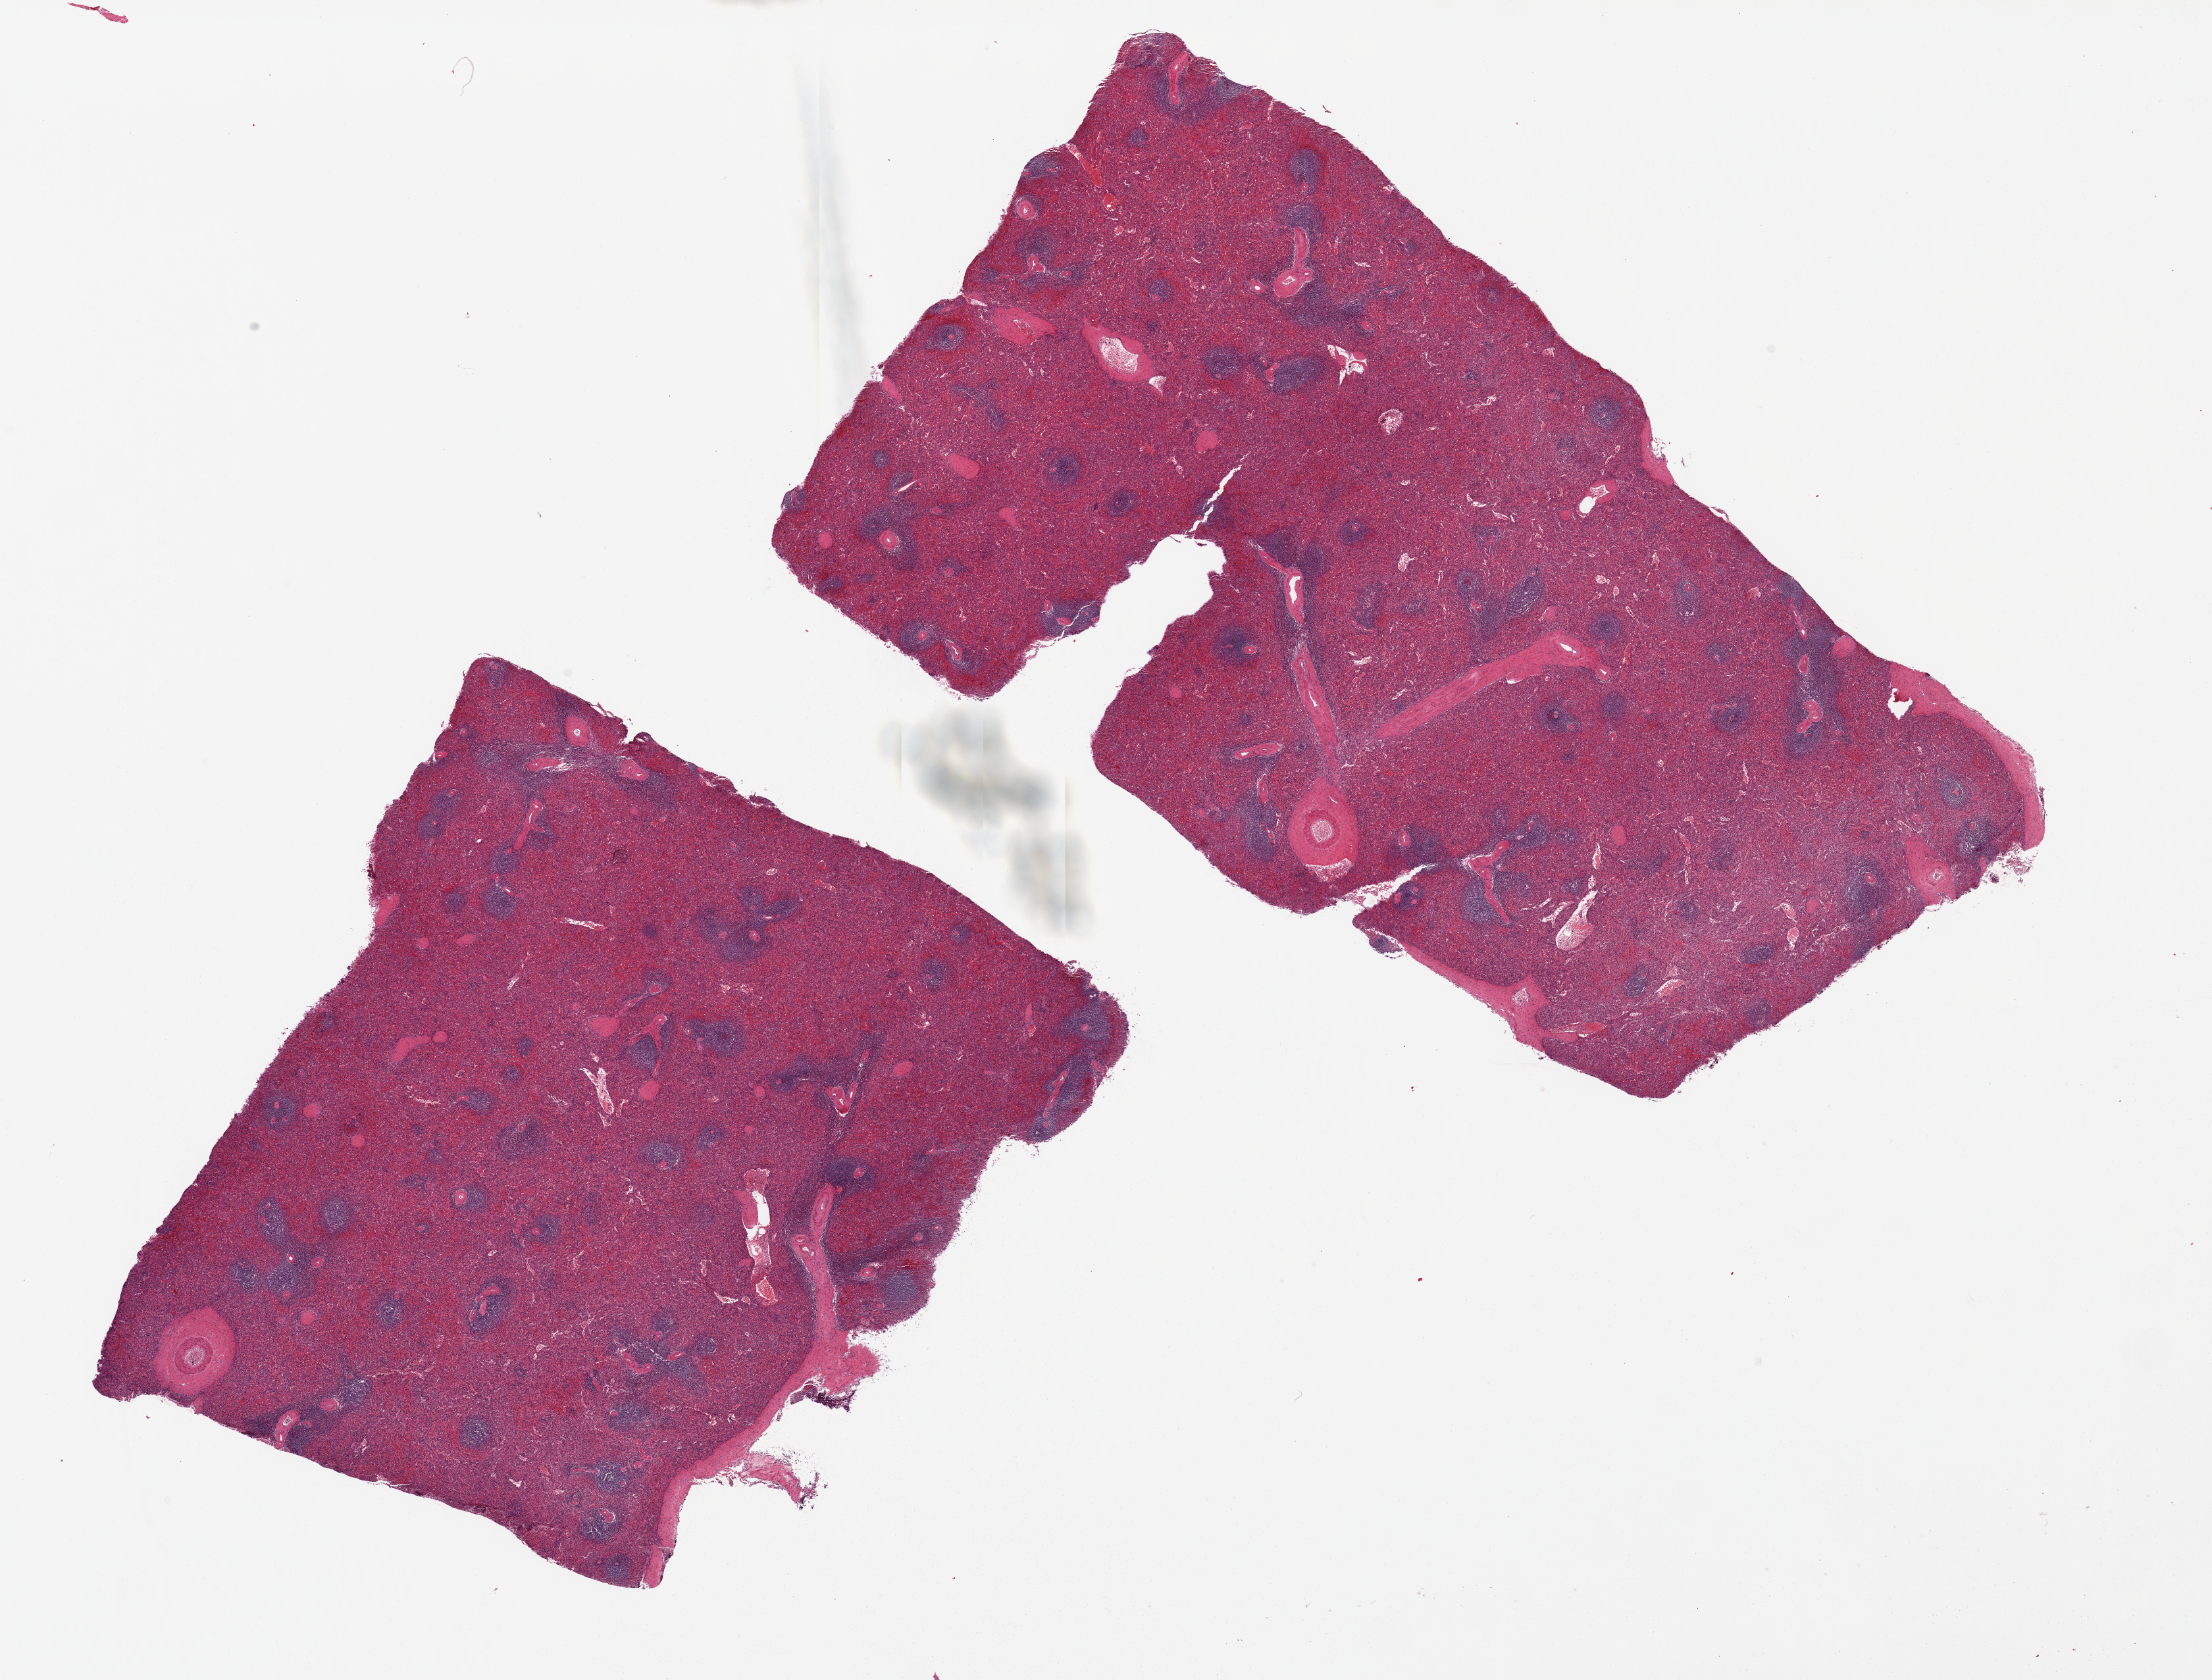
H&E whole-slide image — low-resolution overview of the scanned area, about 26.6 x 20.2 mm (slide scanned at 20x), PAXgene-fixed, paraffin-embedded tissue, sampled site (target tissue): spleen, tissue donor sample.
Pathologist's review note for this sample: 2 pieces; congested.